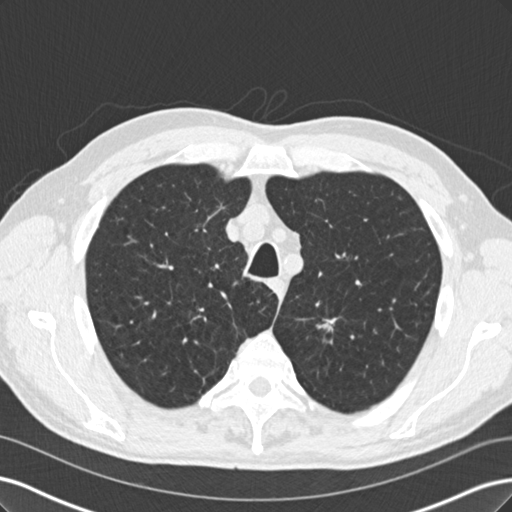
Low-dose screening chest CT, one axial slice. Slice 179 of 219 in the series (ordered by position). Reconstruction kernel B30f. 120 kVp. Lung window (W 1500 / L -600 HU). 512 × 512 image matrix.
Annotated regions visible in this slice (manually delineated by an expert):
- lesion 1 (tumor, upper lobe of left lung): bounding box <316,317,339,333> (left, top, right, bottom; pixels)